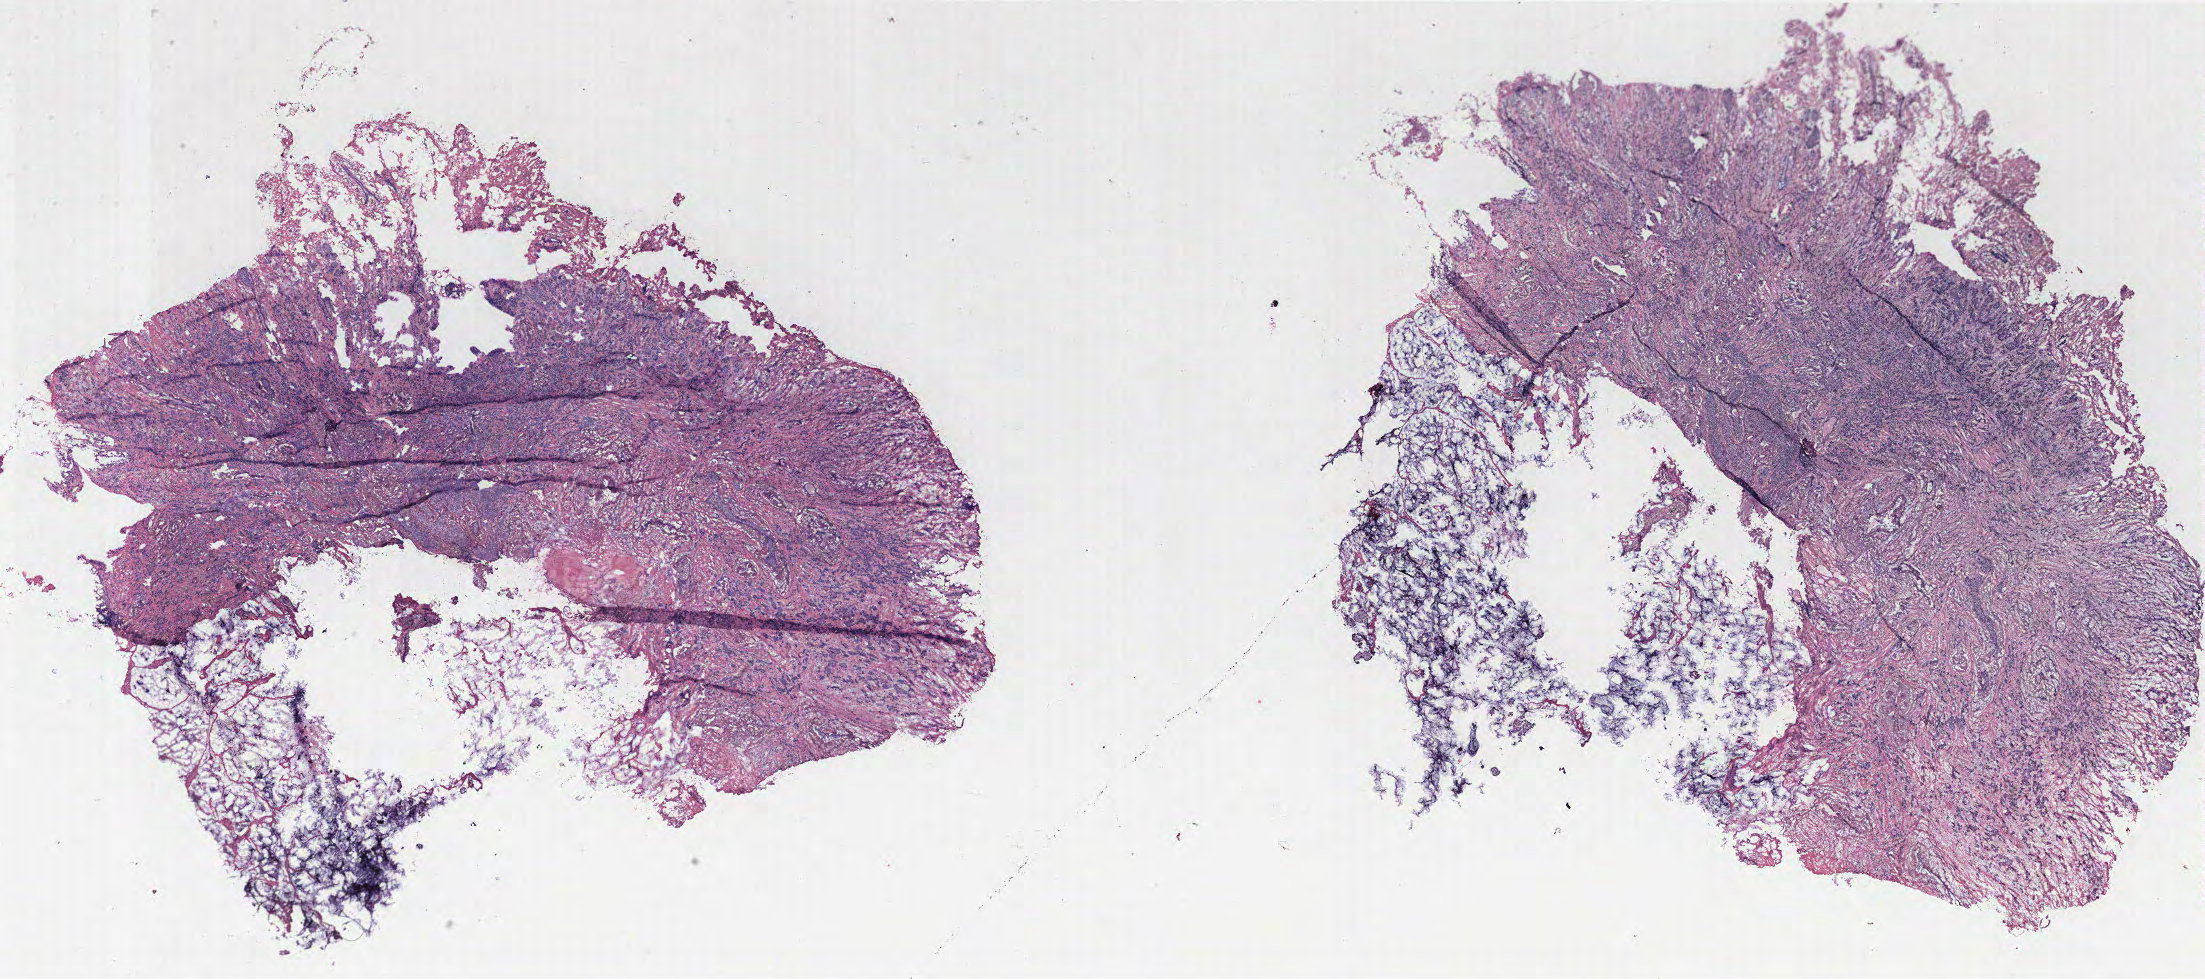
Digitized H&E tissue section (whole slide), low-resolution overview of the scanned area, about 35.3 x 15.7 mm (slide scanned at 40x), breast, tissue type not recorded.
- patient diagnosis (cohort enrolment): breast cancer (breast)